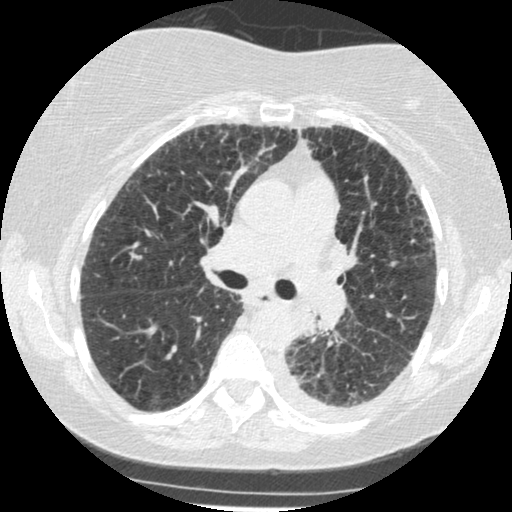
Low-dose screening chest CT, one axial slice. Slice 163 of 341 in the series (ordered by position). Reconstruction kernel STANDARD. 120 kVp. Lung window (W 1500 / L -600 HU). 1.25 mm slice thickness. 512 × 512 image matrix.
Annotated regions visible in this slice (expert manual segmentation):
- lesion 1 (tumor, lower lobe of left lung): bounding box [x1, y1, x2, y2] px = [294, 307, 317, 335]